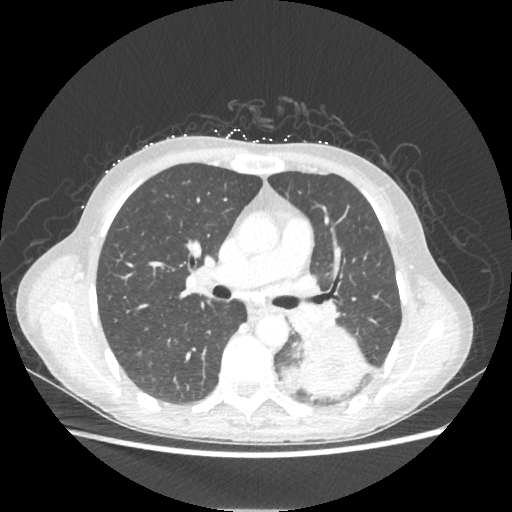
Chest CT, one axial slice; slice 129 of 221 in the series (ordered by position); reconstruction kernel STANDARD; 80 kVp; lung window (W 1500 / L -600 HU); 1.25 mm slice thickness; 512 × 512 image matrix, field of view 360 × 360 mm. Patient: female, 53 years. From the clinical record (not read from this slice): clinical TNM (as recorded): T3 N0 M0.
Annotated regions visible in this slice (bounding box drawn by a radiologist):
- lung tumour (recorded histology: adenocarcinoma): bounding box [x1, y1, x2, y2] px = [276, 325, 371, 397]